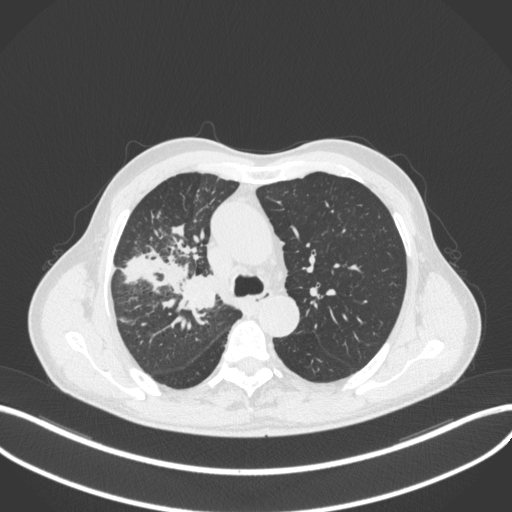
Chest CT, one axial slice. Position 332 of 490 along the scan axis. Reconstruction kernel B31f. Lung window (W 1500 / L -600 HU). 512 × 512 image matrix. Patient: male, 69 years. Case-level facts recorded for this patient, not image findings: clinical TNM (as recorded): T2a N0 M0.
Annotated regions visible in this slice (rectangle marked by the reading radiologist):
- lung tumour (recorded histology: adenocarcinoma): bounding box [x1, y1, x2, y2] px = [176, 275, 224, 315]